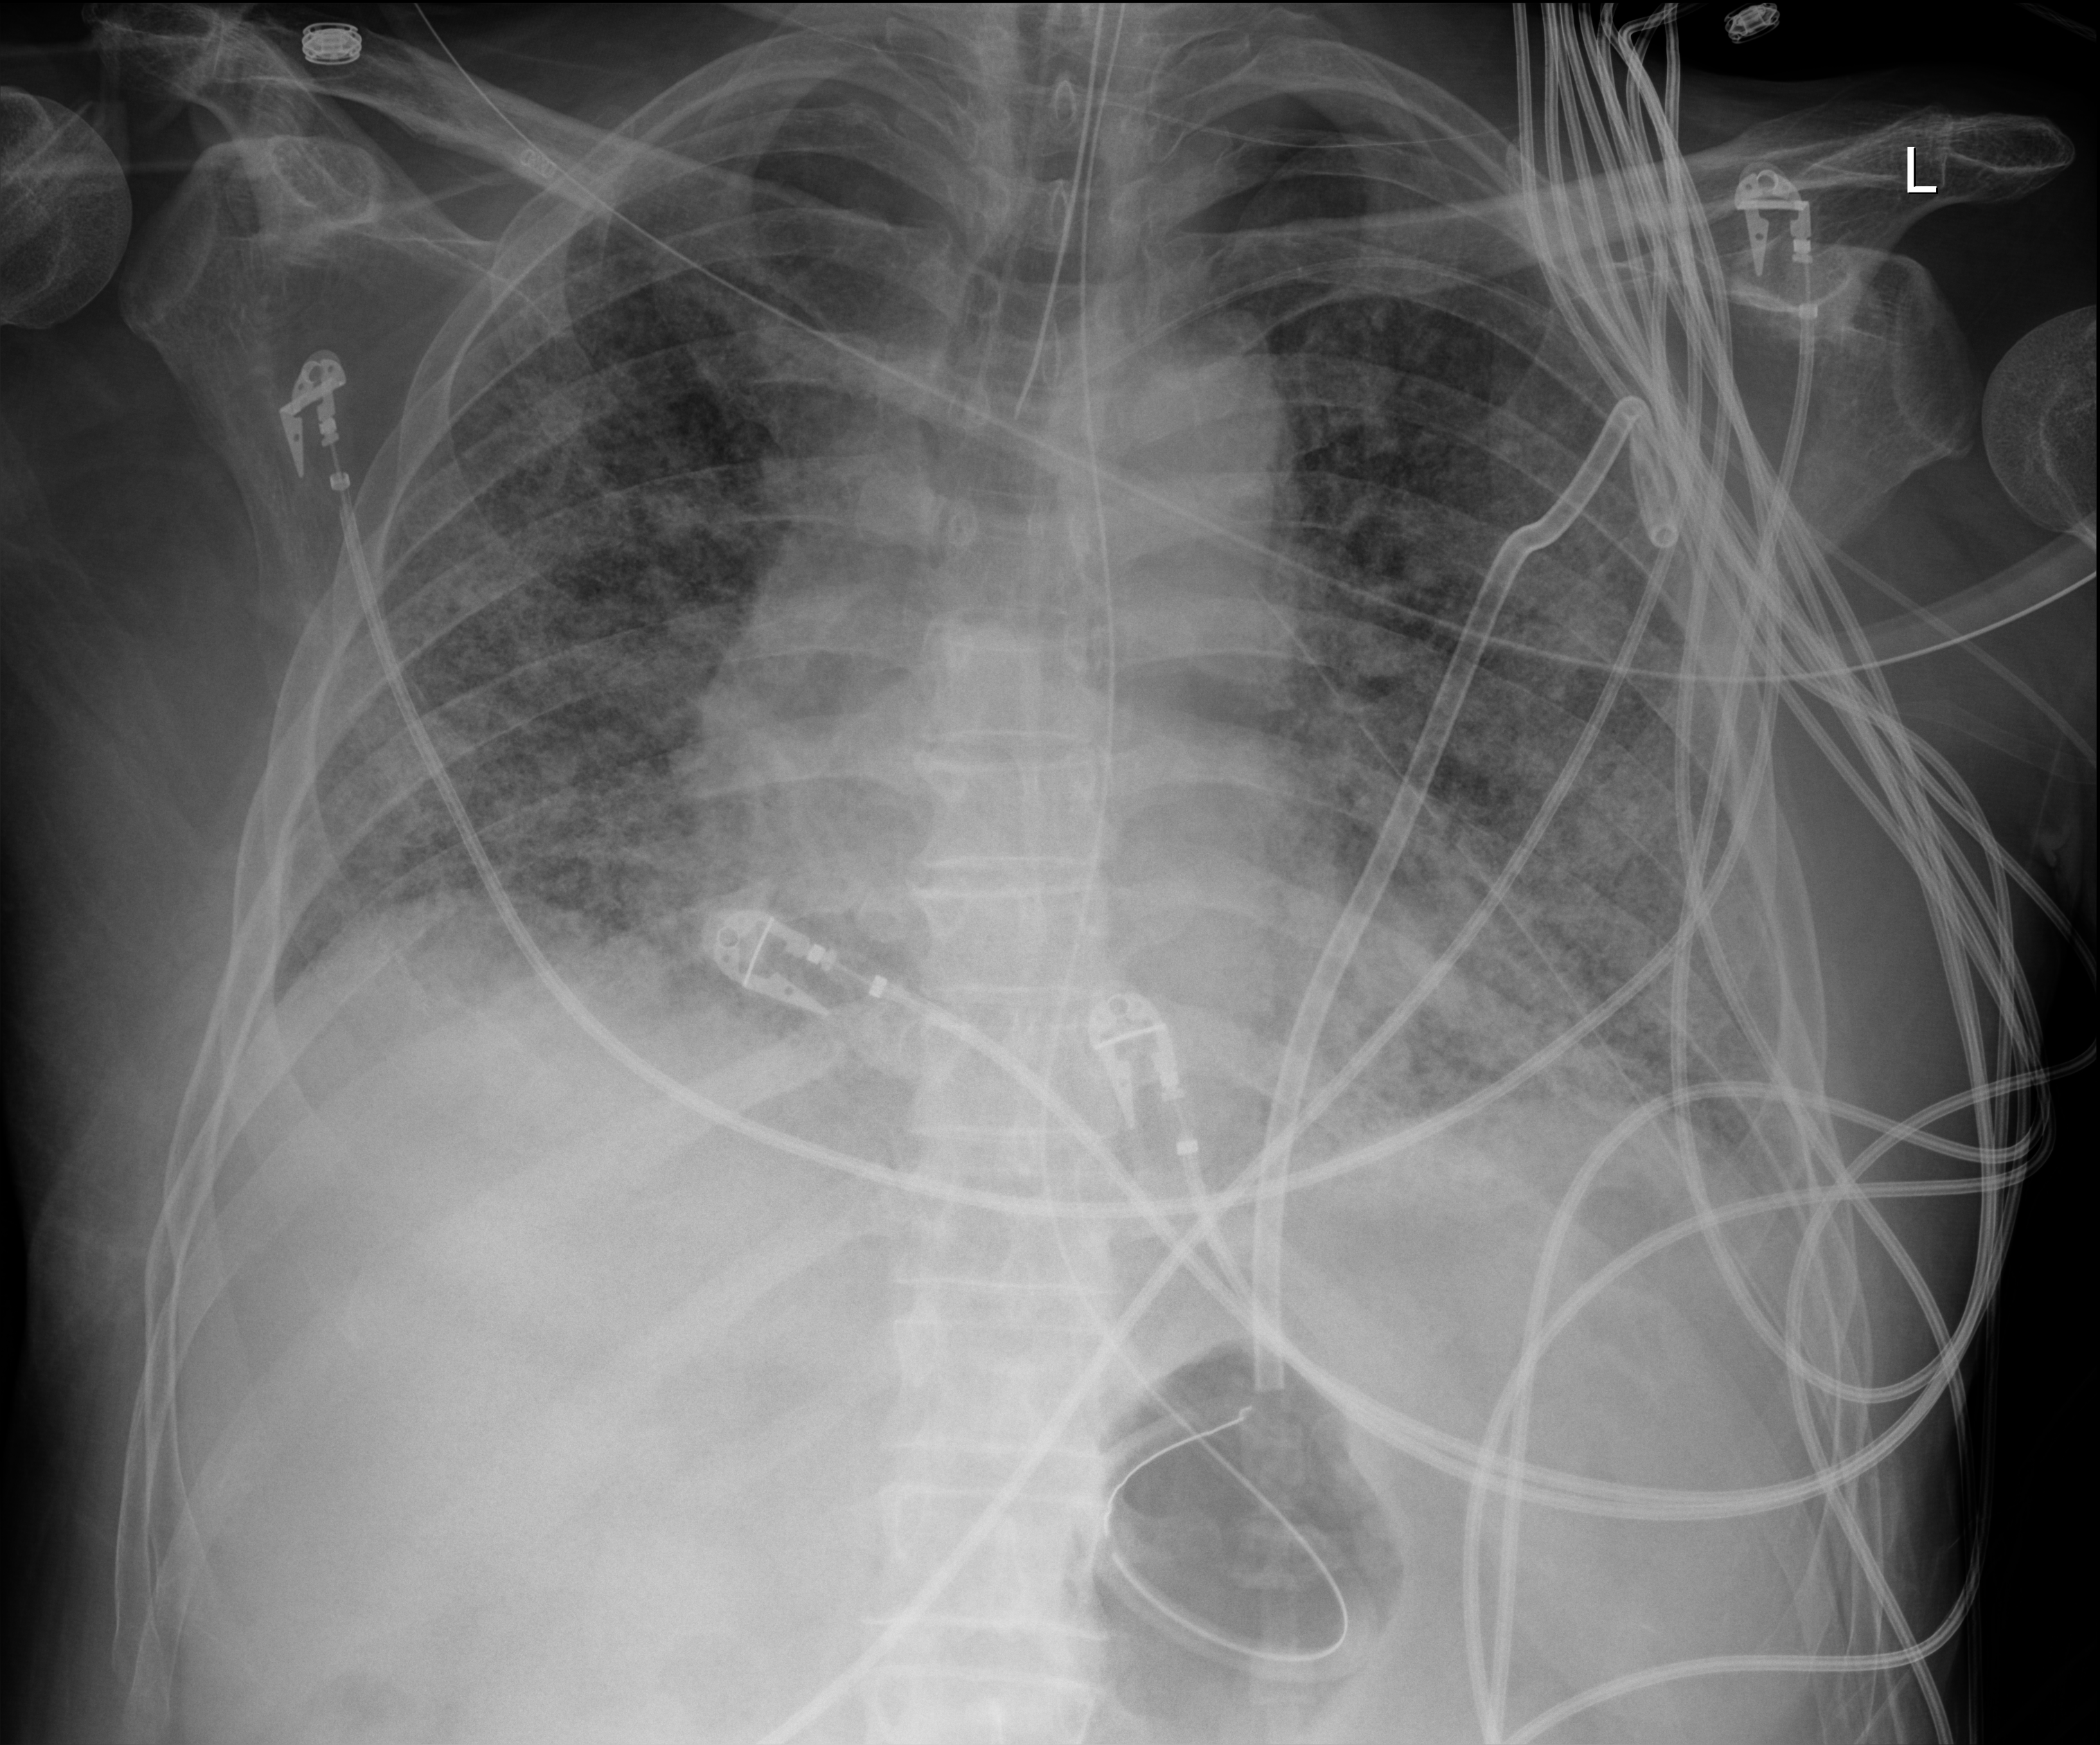
Chest X-ray; anteroposterior (AP) projection. Male patient hospitalised with COVID-19, age 60–74 years.
Admission-level facts for this patient (not findings on this image; timing relative to this image not recorded): admitted to intensive care during this hospital stay: yes; mechanically ventilated during this hospital stay: yes.